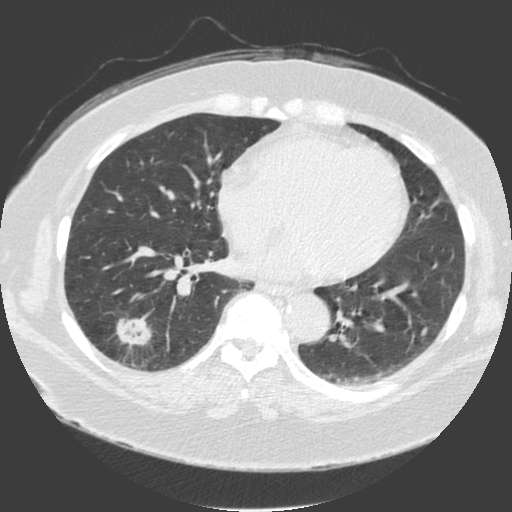
Low-dose screening chest CT, one axial slice; lung window (W 1500 / L -600 HU); 2 mm slice thickness; 512 × 512 image matrix, field of view 370 × 370 mm.
Annotated regions visible in this slice (expert manual segmentation):
- lesion 1 (tumor, lower lobe of right lung): bounding box <117,315,151,347> (left, top, right, bottom; pixels)